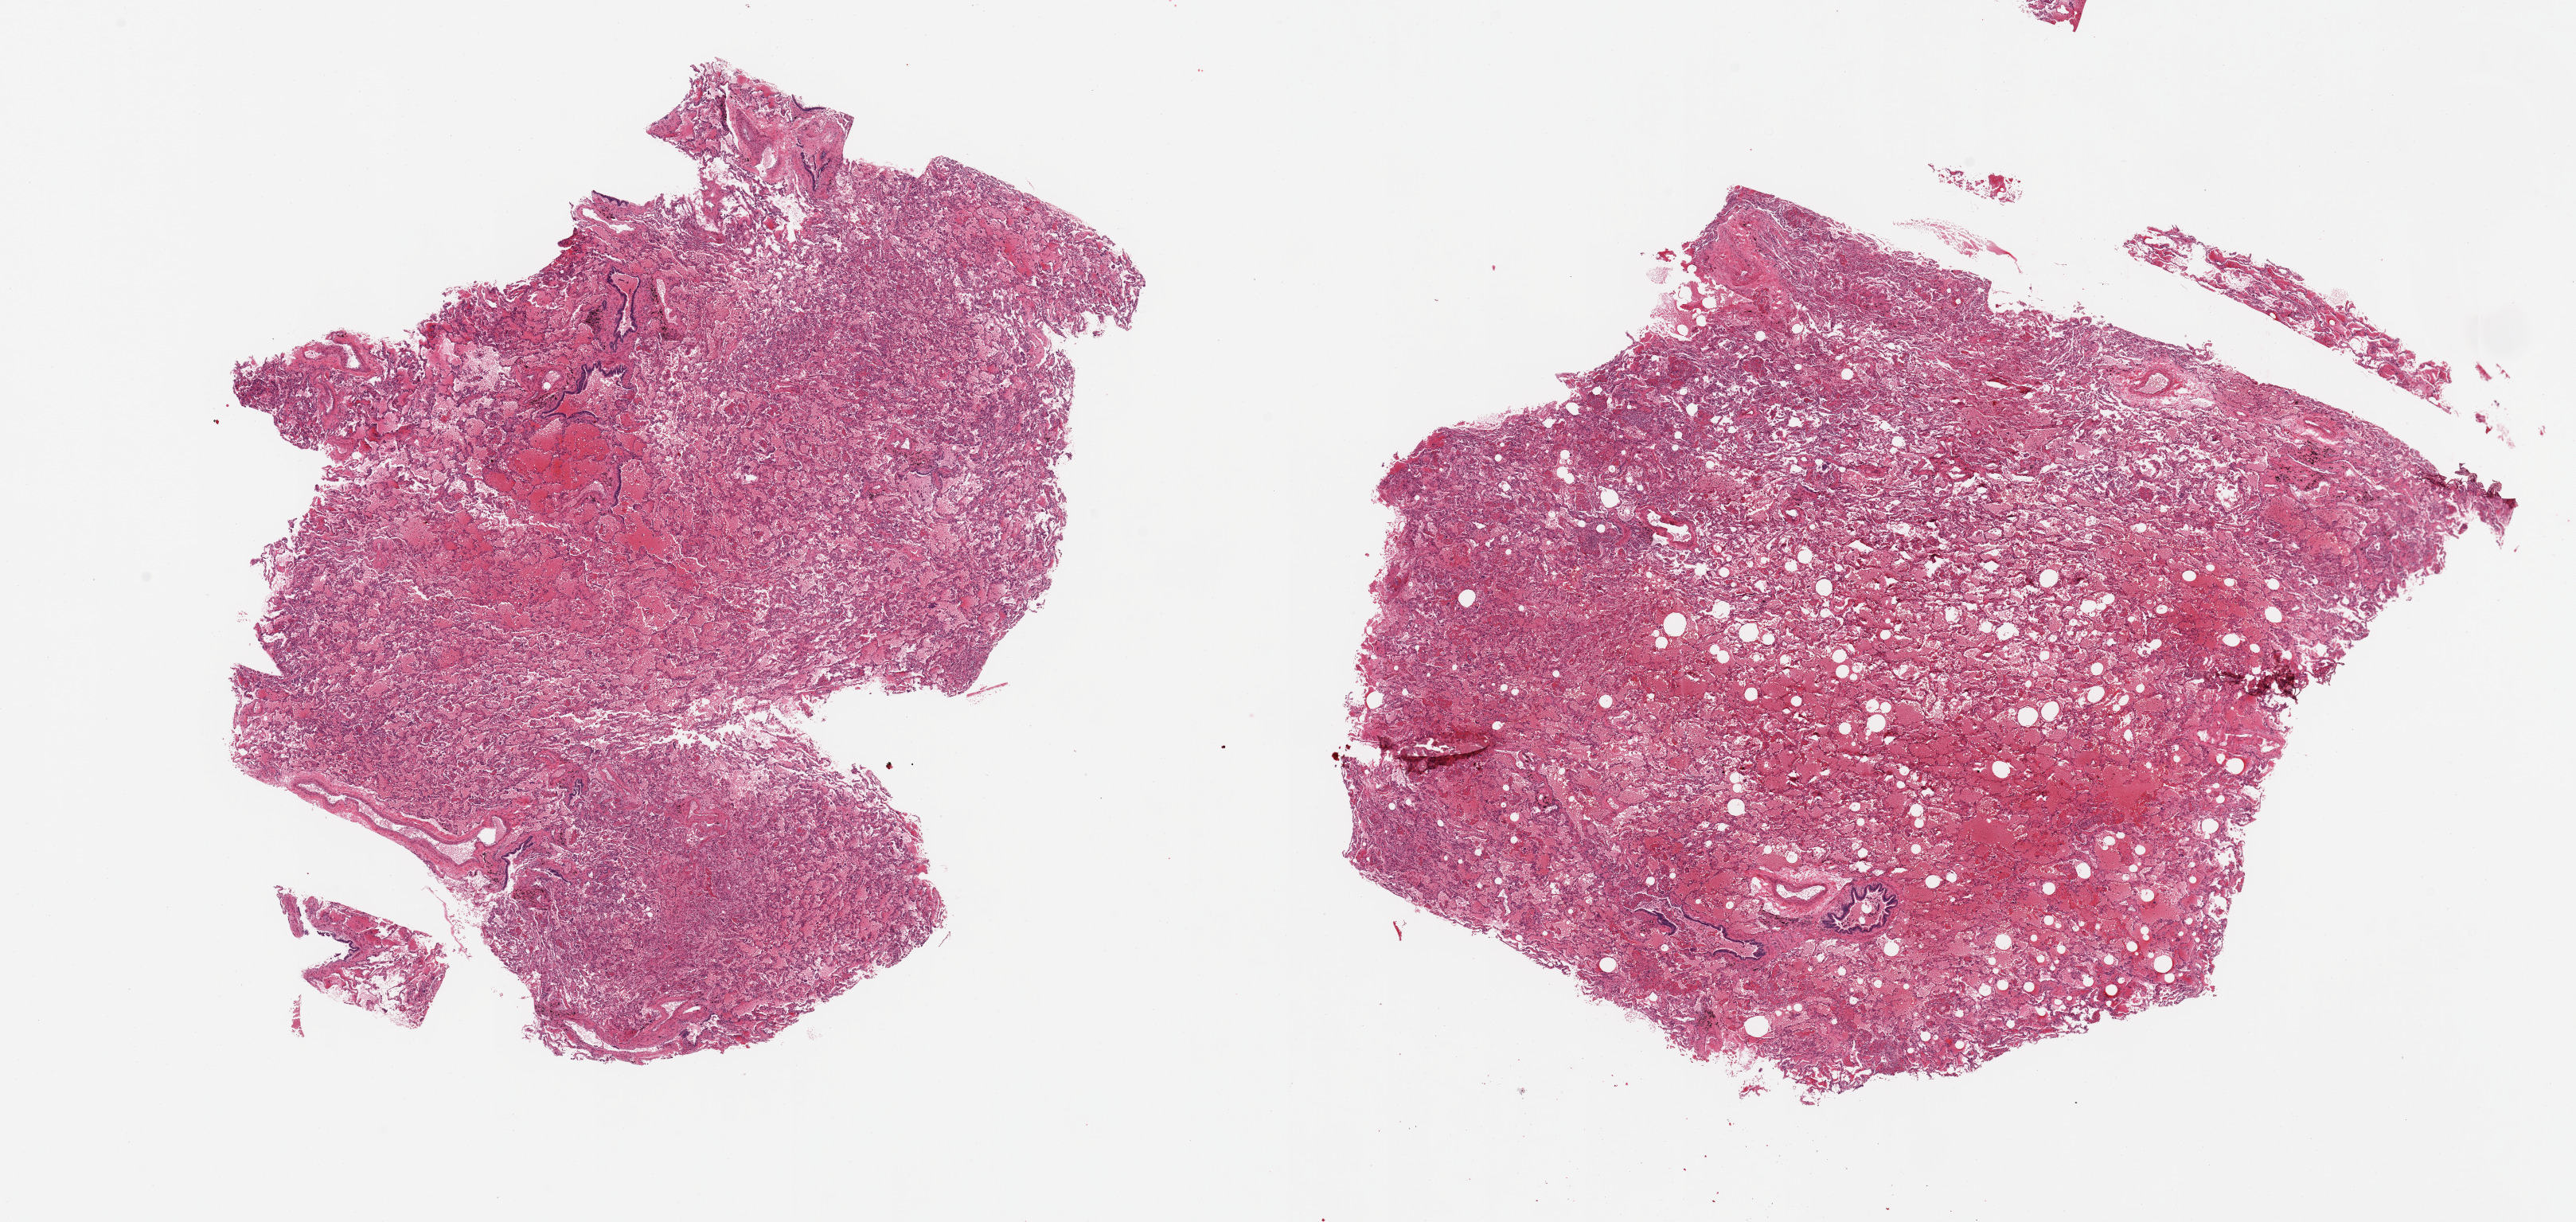
Whole-slide image, hematoxylin and eosin (H&E) stain — whole scanned area (about 25.6 x 12.1 mm) shown as a low-resolution overview, PAXgene-fixed paraffin-embedded (PFPE) section, sampled site (target tissue): lung, tissue donor sample. Male donor.
- pathologist's review note for this sample: 2 pieces, diffuse chronic and subacute marked congestion. Patchy bronchial metaplasia